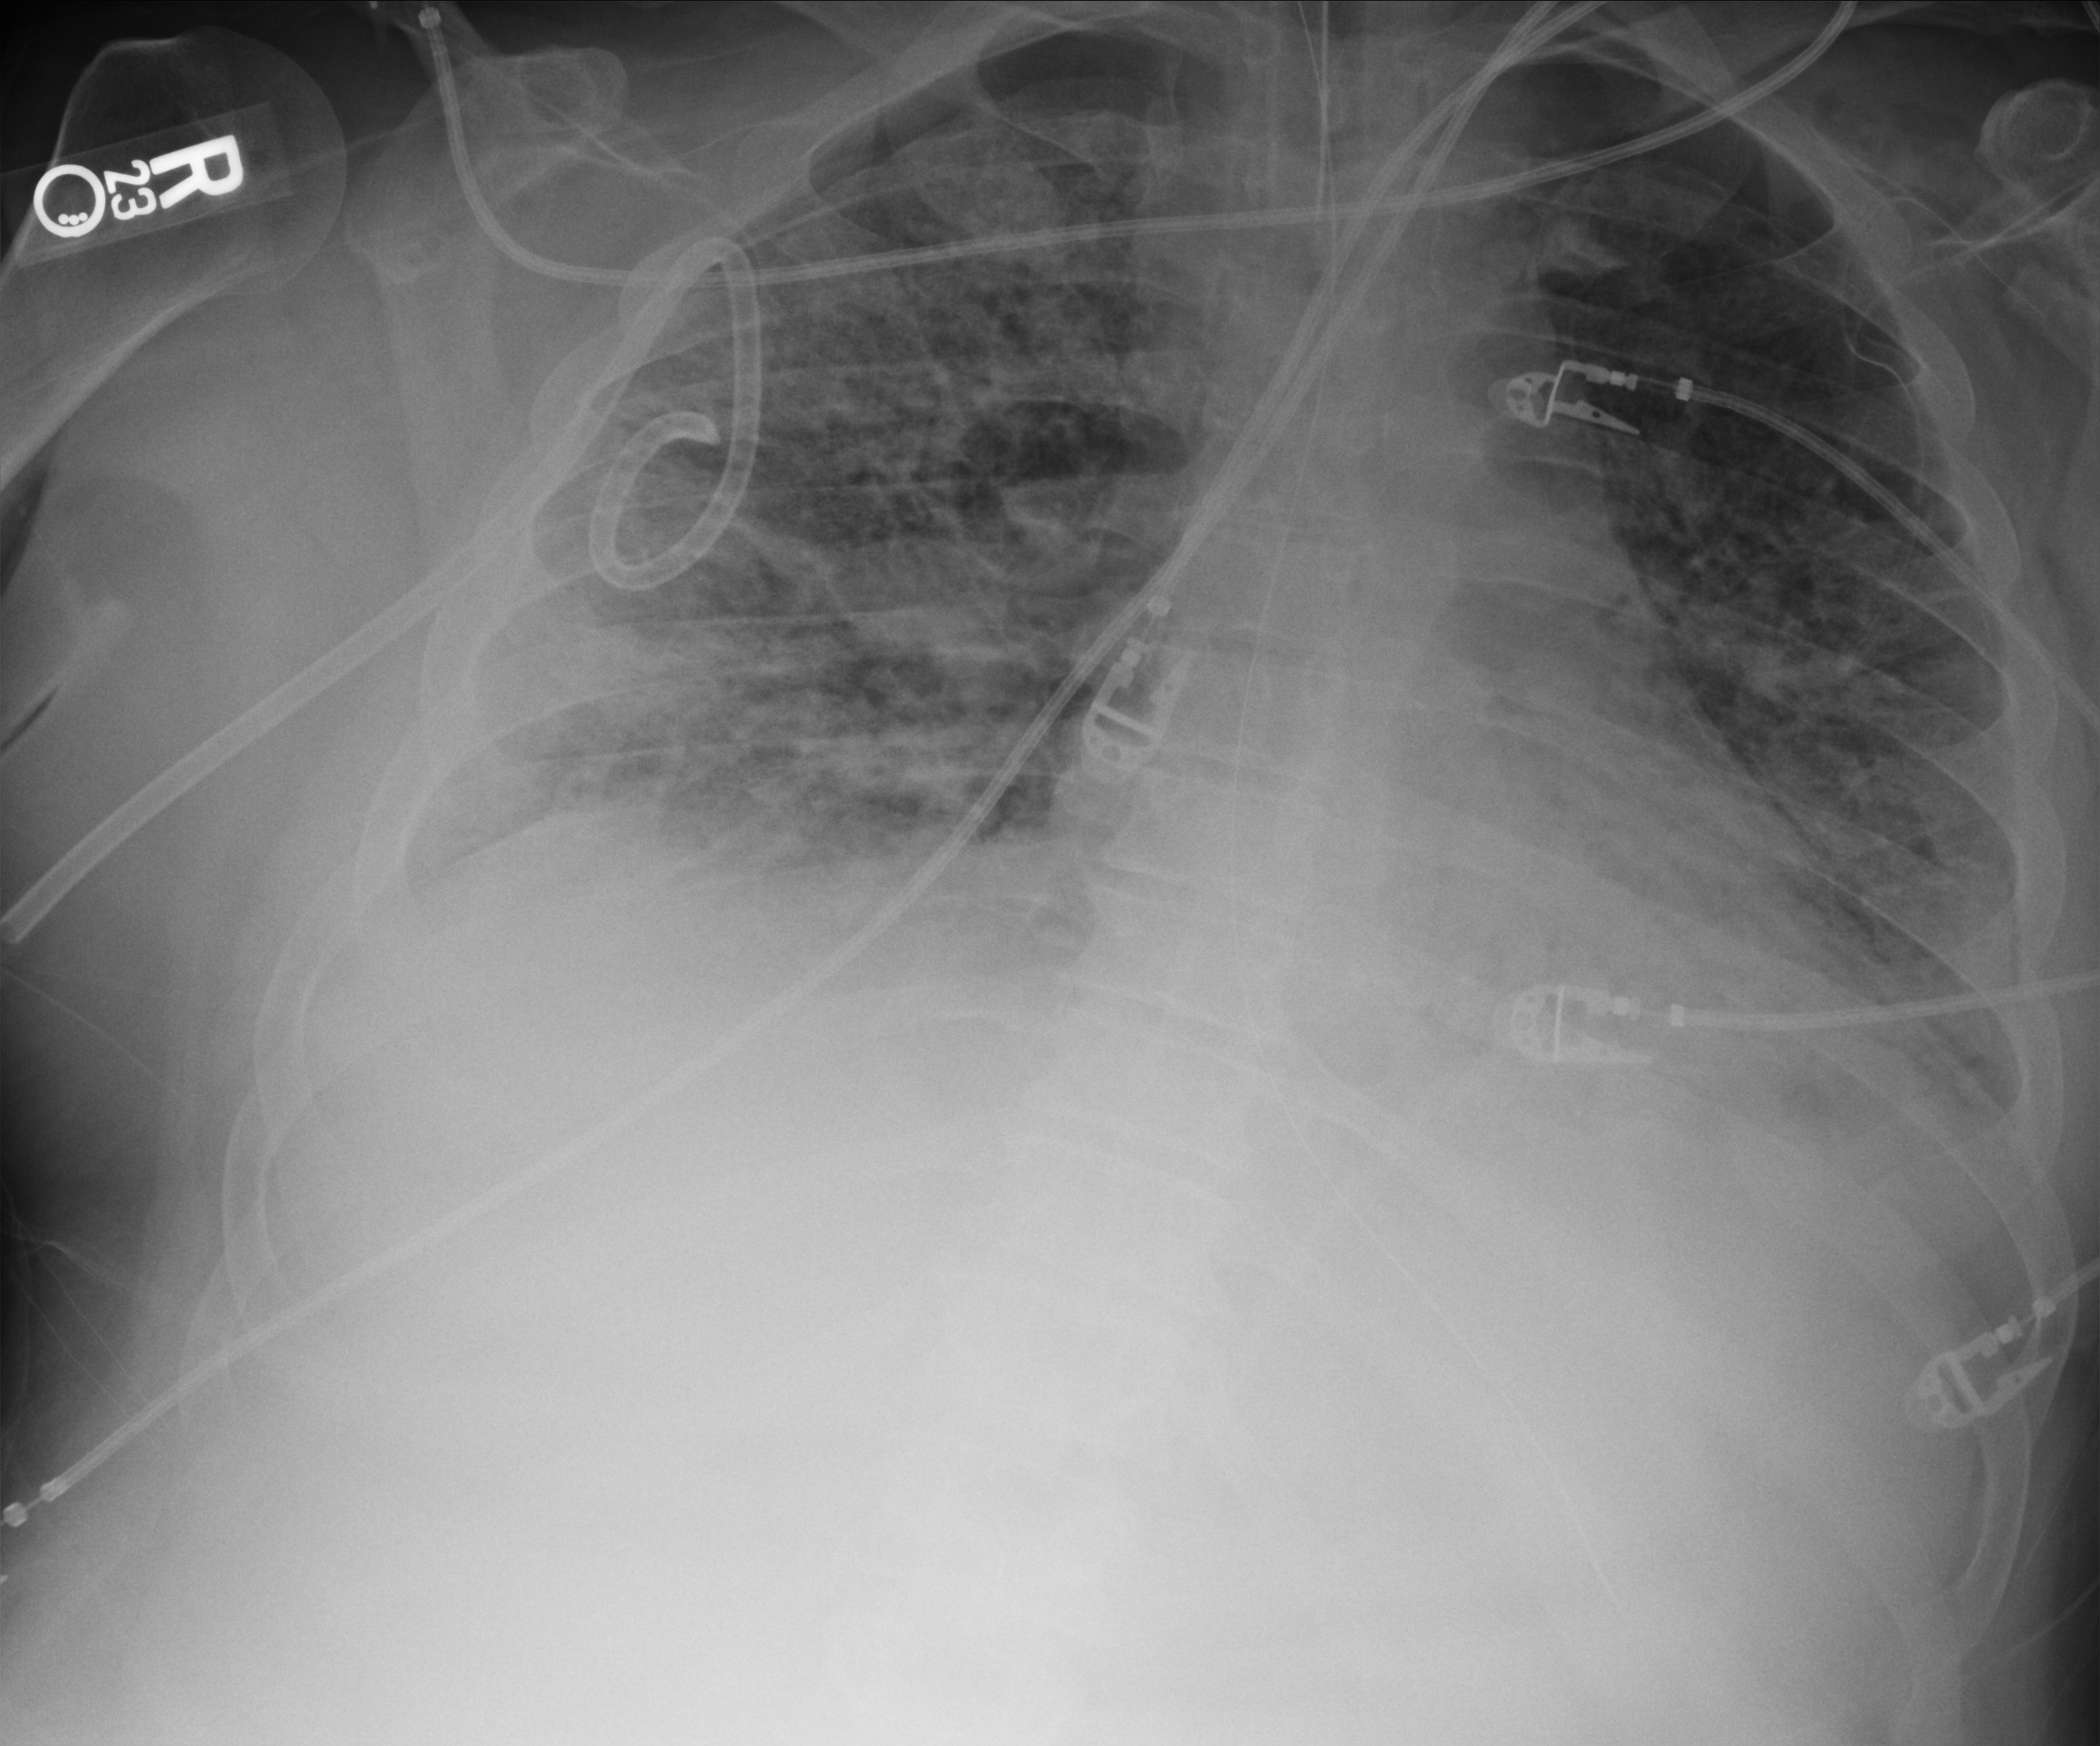
Portable chest radiograph. Adult patient hospitalised with COVID-19, age 18–59 years.
Hospital-stay facts (about this admission, not read from this image; timing relative to this image not recorded): admitted to intensive care during this hospital stay: yes; mechanically ventilated during this hospital stay: yes.